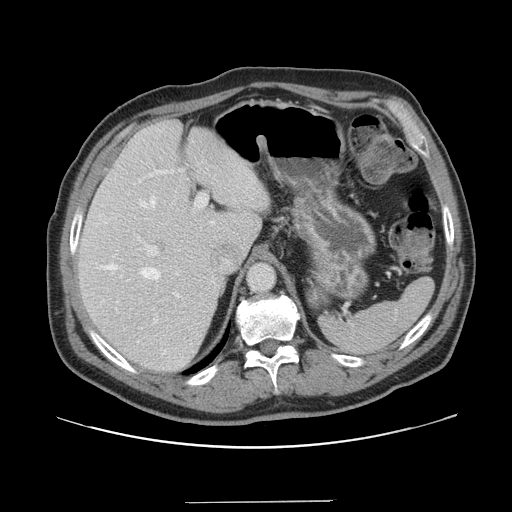
Contrast-enhanced abdominal CT, one axial slice; slice 107 of 151 in the series (ordered by position); intravenous contrast given; soft-tissue window (W 400 / L 40 HU); 2.5 mm slice thickness; 512 × 512 image matrix, field of view 399 × 399 mm. Male patient, age 63 years. Case-level facts recorded for this patient, not image findings: diagnosis: colorectal cancer liver metastases, imaged before liver resection; multiple liver metastases: no; largest metastasis: 2.1 cm; disease in both lobes: no.
Structures marked on this image (expert manual segmentation):
- hepatic veins: bounding box [x1, y1, x2, y2] px = [102, 196, 214, 280]
- liver: [78, 120, 270, 373]
- planned liver remnant (the part of the liver to remain after resection): [78, 120, 263, 373]
- portal vein (with intrahepatic branches): [144, 169, 208, 298]